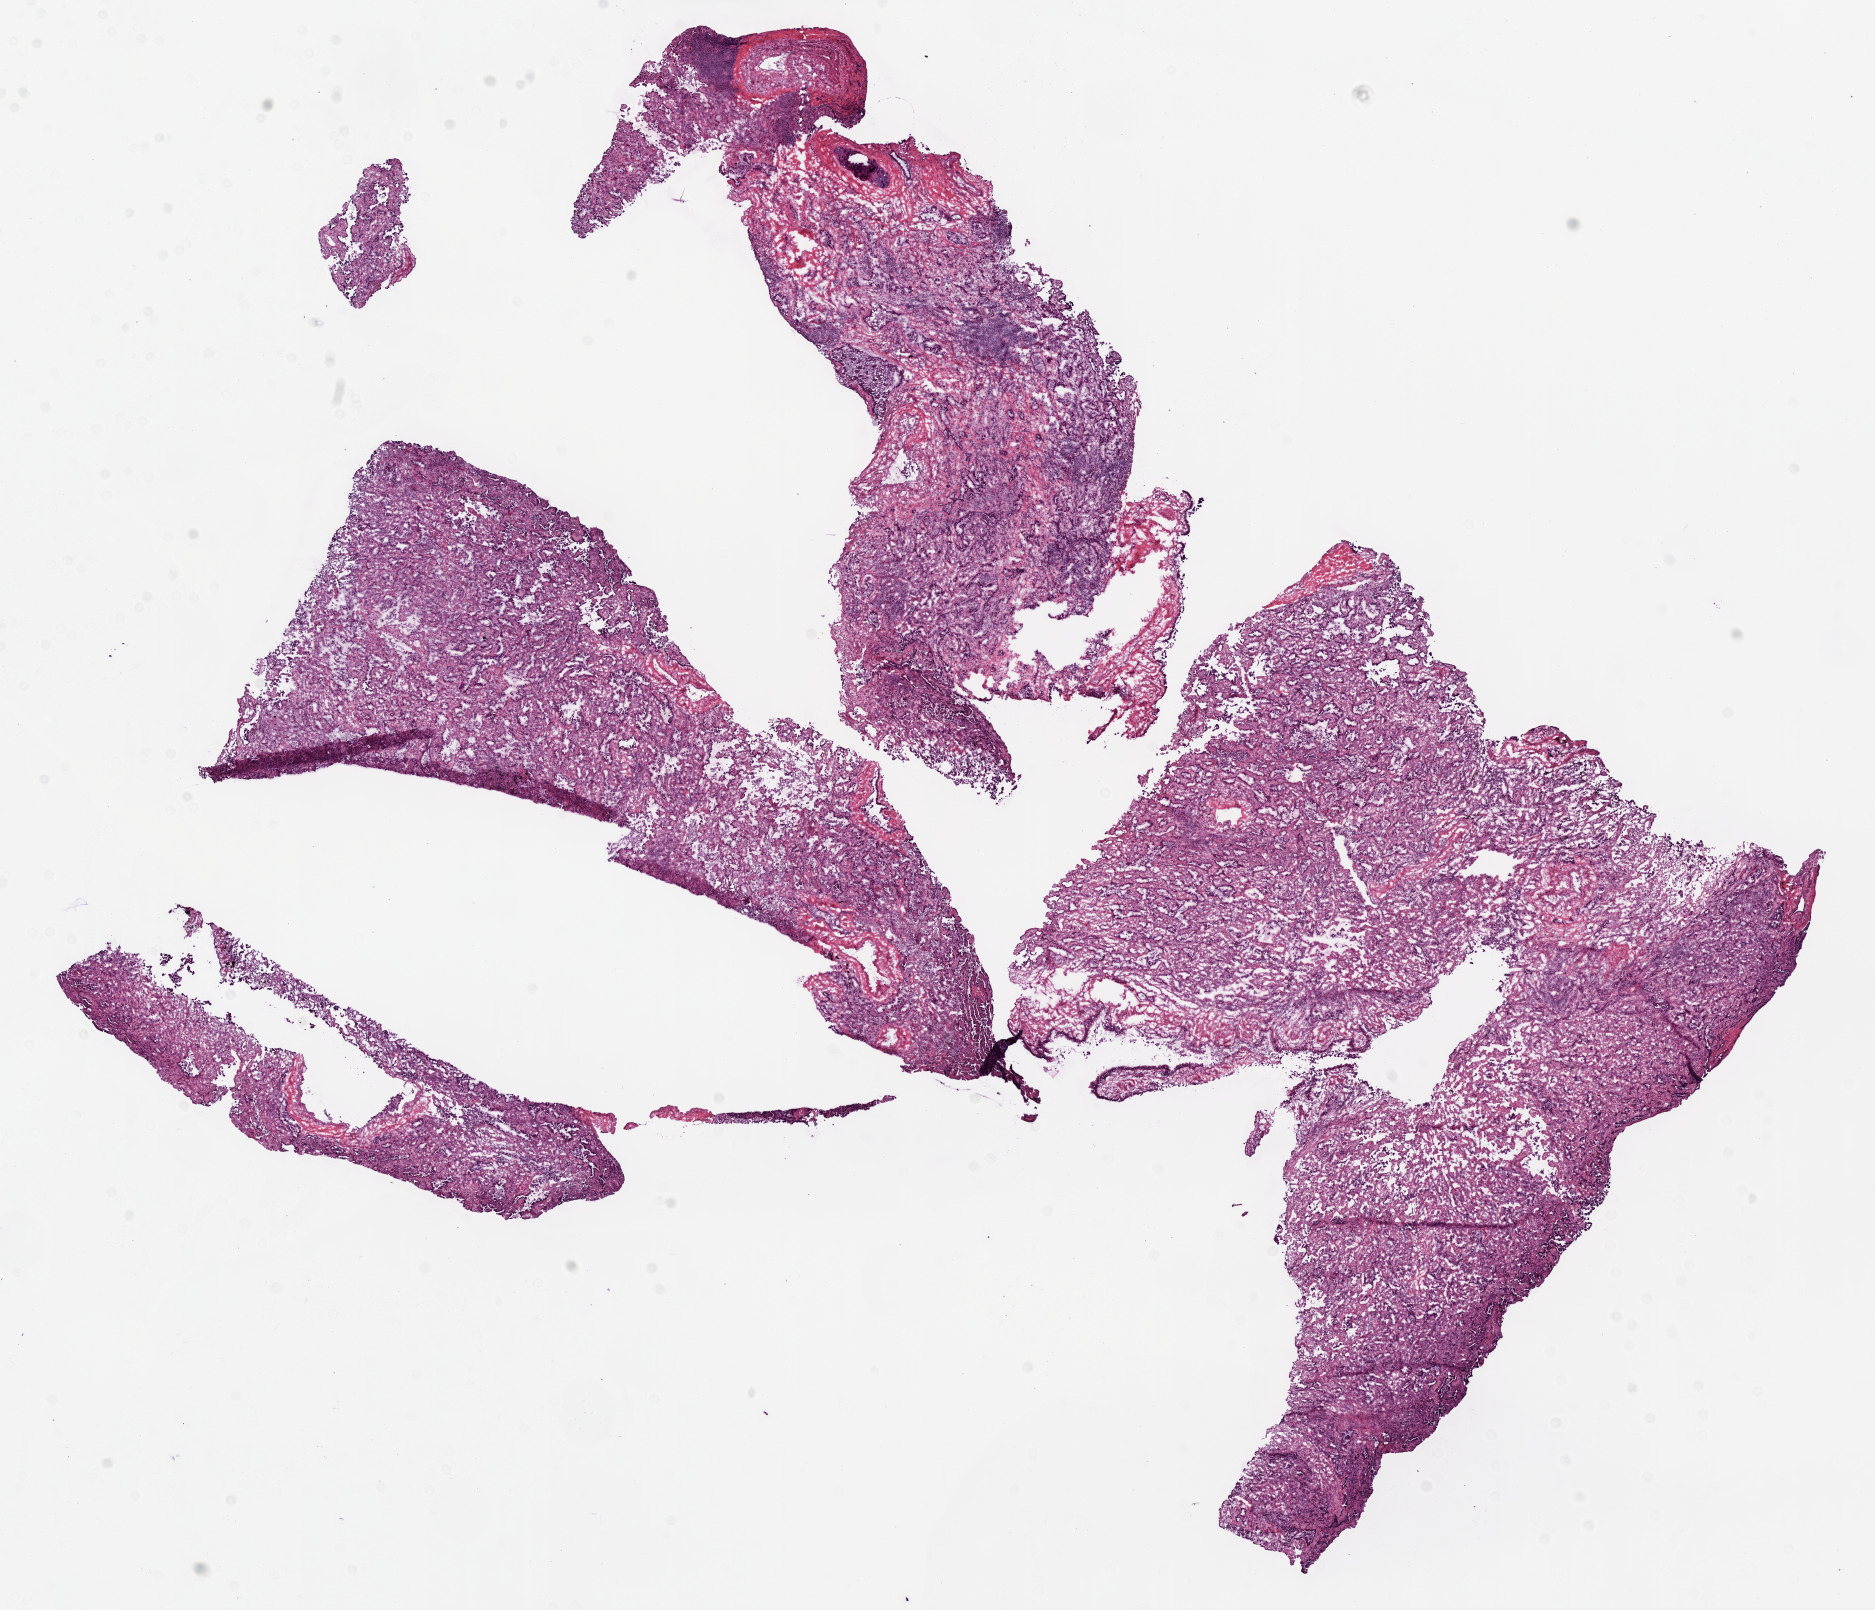
Whole-slide histology image, Hematoxylin and eosin (H&E) stained, a low-resolution overview of the entire scanned area, about 15.0 x 12.9 mm (from a 20x scan), frozen section from the bottom of the tissue portion, lung, primary tumour sample. Female, age 61 years at initial diagnosis. Composition of this section per pathologist review: tumour cells 30%, tumour nuclei 60%, normal cells 0%, stromal cells 40%, necrosis 30%. Infiltration values recorded for this section: lymphocyte infiltration 90%, monocyte infiltration 4%, neutrophil infiltration 5%.
- TNM: T1 N0 M0
- AJCC pathologic stage: IA
- pathologic diagnosis: Adenocarcinoma, NOS